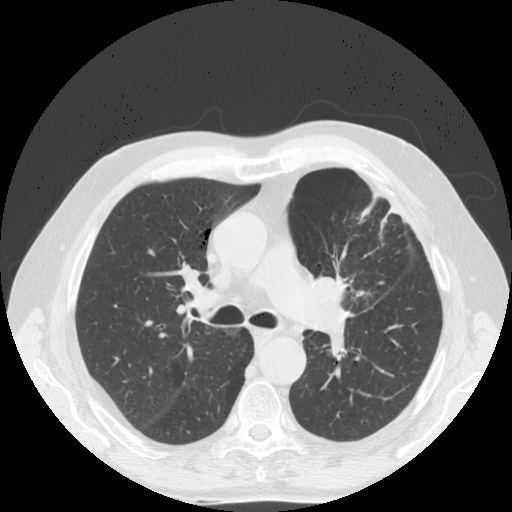
Low-dose screening chest CT, one axial slice; reconstruction kernel STANDARD; 140 kVp; lung window (W 1500 / L -600 HU); 2.5 mm slice thickness; 512 × 512 image matrix, field of view 380 × 380 mm.
Annotated regions visible in this slice (expert manual segmentation):
- lesion 1 (tumor, upper lobe of left lung): bounding box (x1, y1, x2, y2) in pixels: (312, 277, 337, 299)